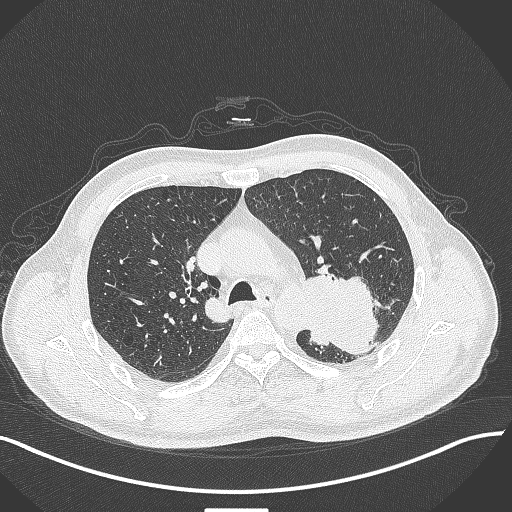
Chest CT, one axial slice. Slice 294 of 429 in the series (ordered by position). 120 kVp. Lung window (W 1500 / L -600 HU). 512 × 512 image matrix, field of view 400 × 400 mm. Male patient, age 55 years. Case-level facts recorded for this patient, not image findings: clinical TNM (as recorded): T3 N0 M1c.
Annotated regions visible in this slice (bounding box drawn by a radiologist):
- lung tumour (recorded histology: adenocarcinoma): bounding box [x1, y1, x2, y2] px = [302, 268, 383, 366]